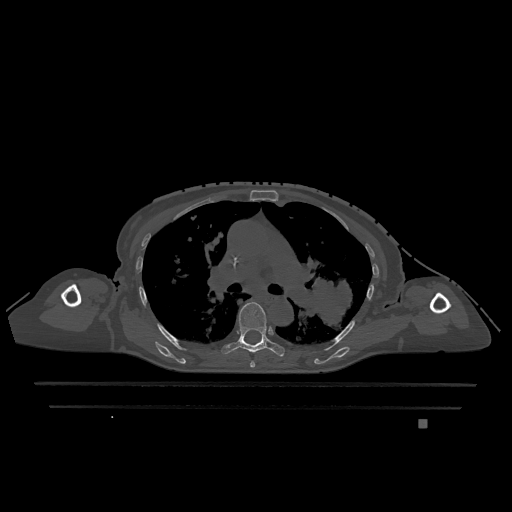
CT including the spine, one axial slice. Slice 794 of 1317 in the series (ordered by position). Bone window (W 1800 / L 400 HU). 0.5 mm slice thickness. 512 × 512 image matrix, field of view 500 × 500 mm. Female patient, age 74 years. Case-level facts recorded for this patient, not image findings: primary cancer: lung; vertebrae with lytic lesions (as recorded): T1, T4, T5, T6, L4, L5.
Annotated regions visible in this slice (semi-automatic segmentation, software-assisted and operator-edited):
- T5 vertebra: bounding box [x1, y1, x2, y2] px = [250, 361, 255, 368]
- T6 vertebra: [222, 302, 285, 357]